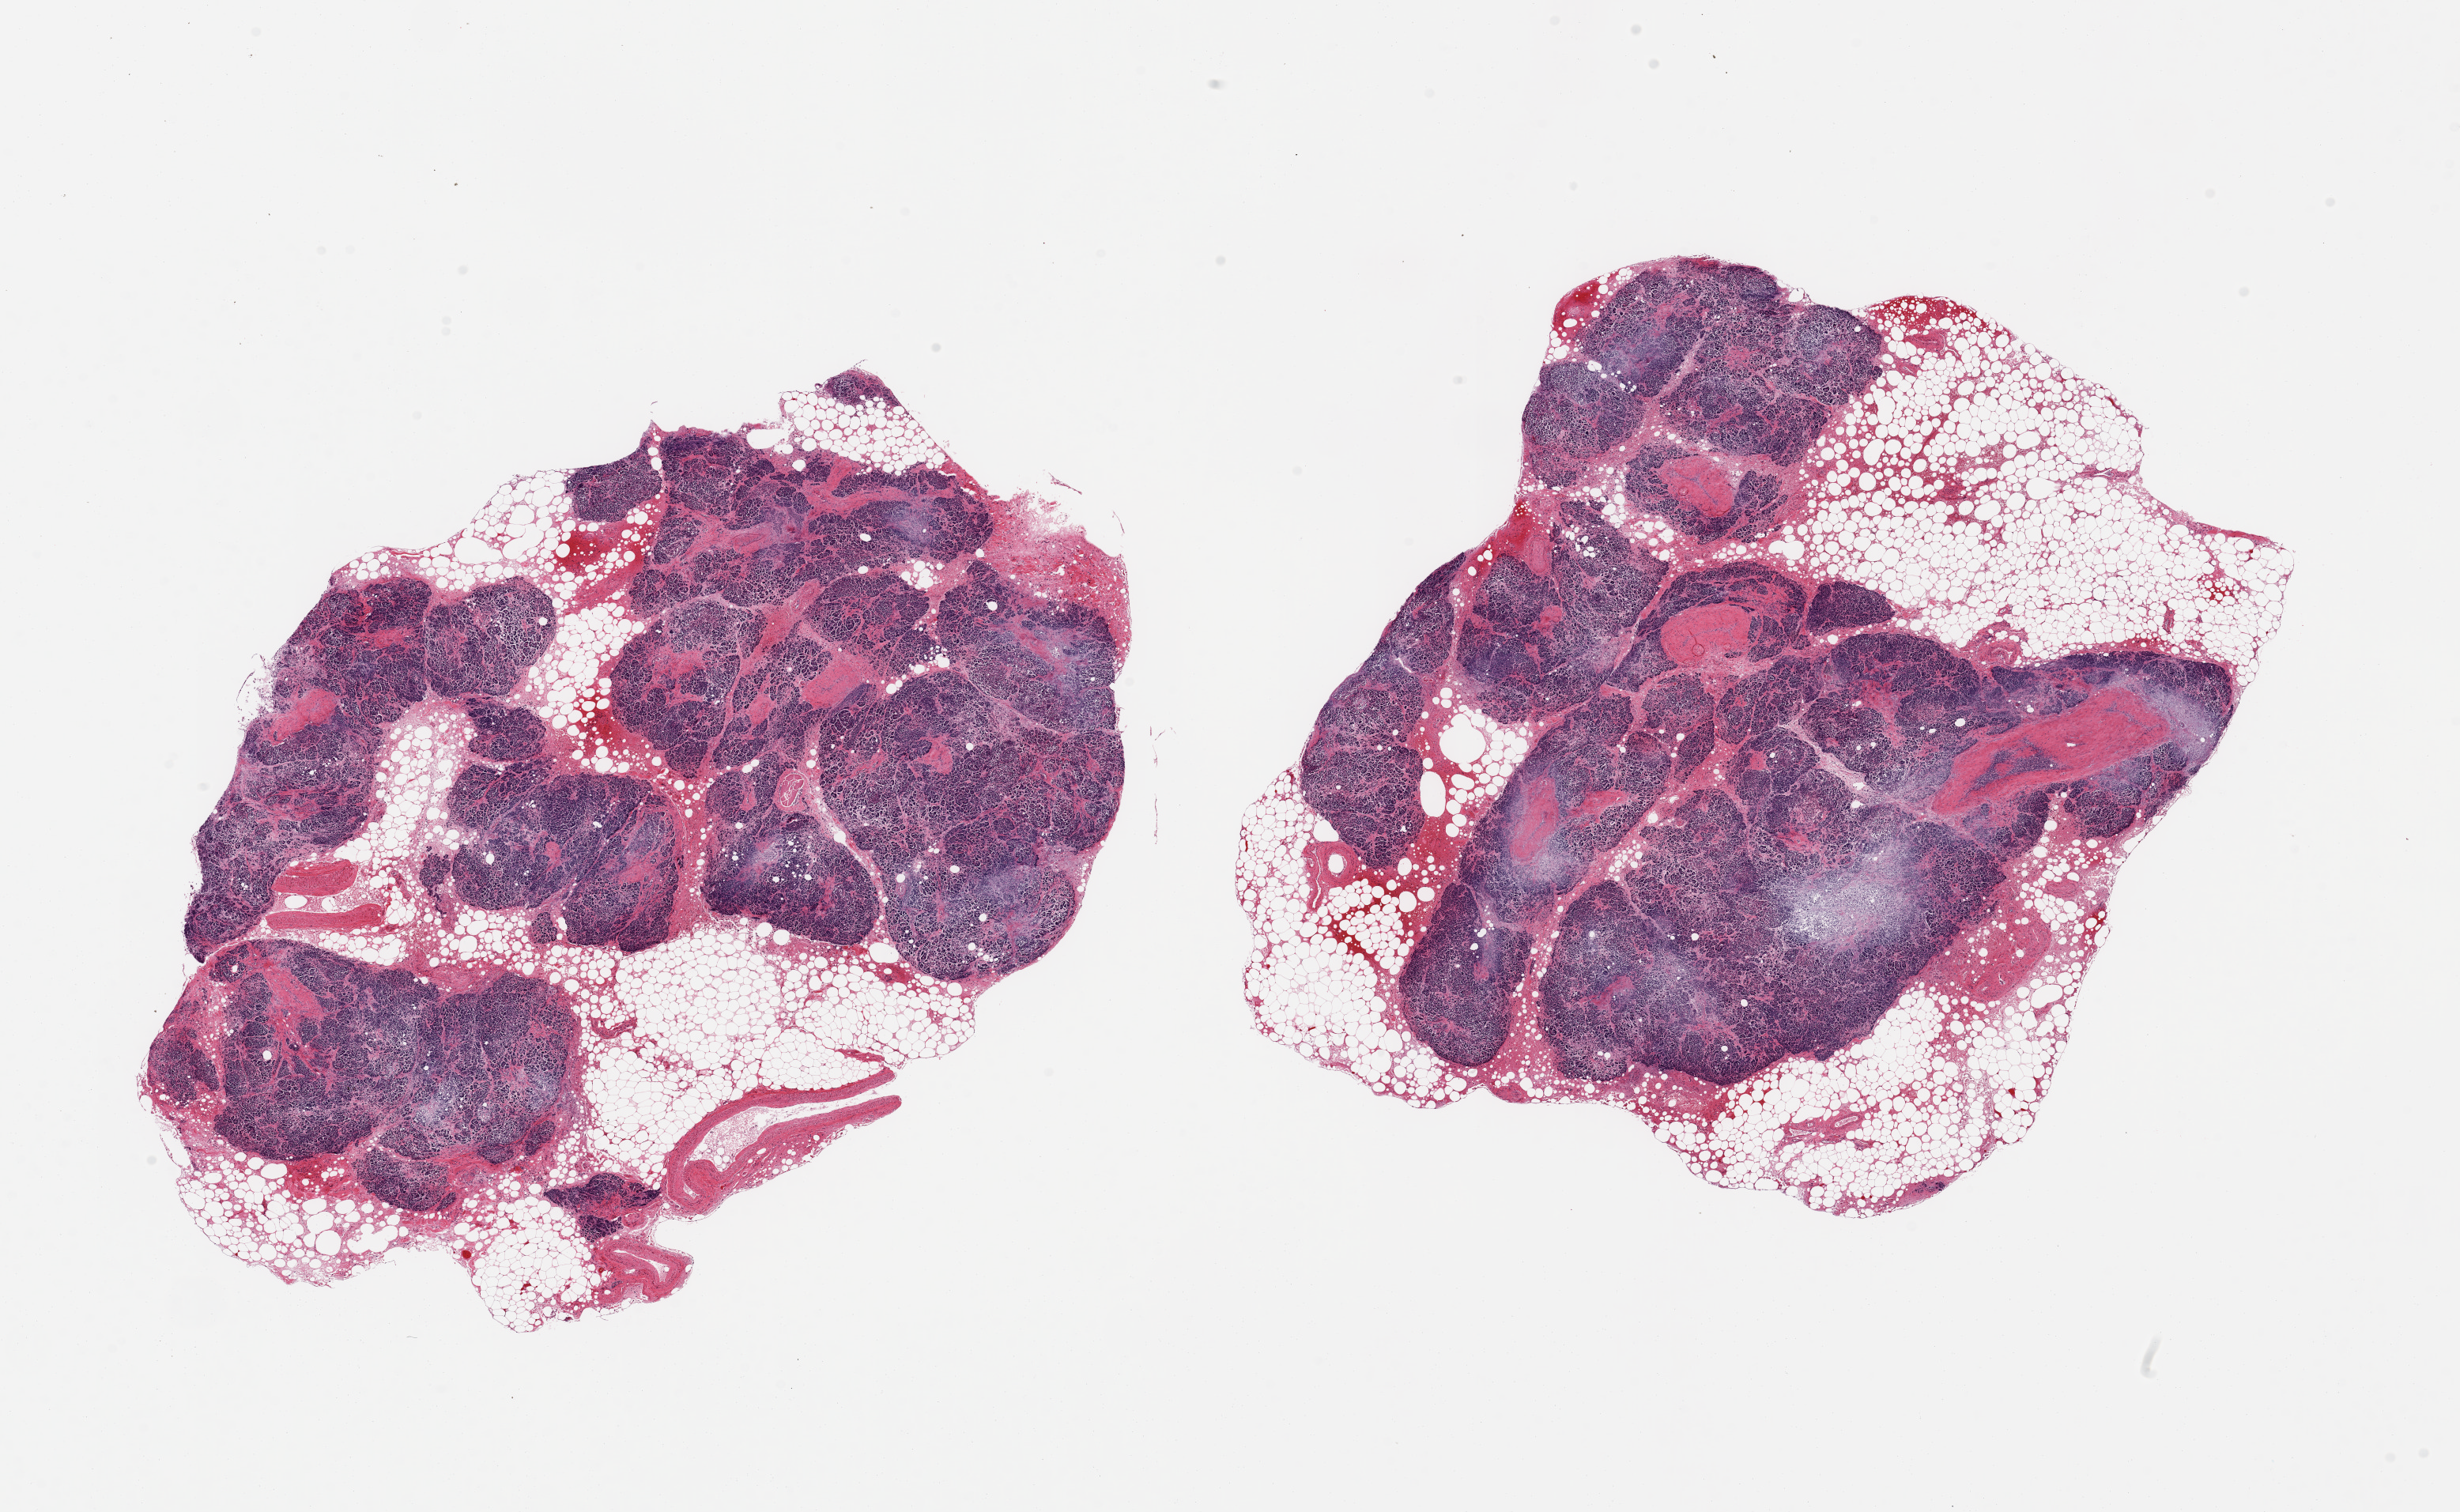
Hematoxylin and eosin (H&E) whole-slide image — shown as a low-resolution overview of the whole scanned area (about 24.6 x 15.1 mm). PAXgene-fixed paraffin-embedded (PFPE) section. Sampled site (target tissue): pancreas. Donor tissue sample. Donor sex: male.
Reviewer comment on this tissue sample: 2 pieces; some foci of moderate autolysis; 30% internal fat.